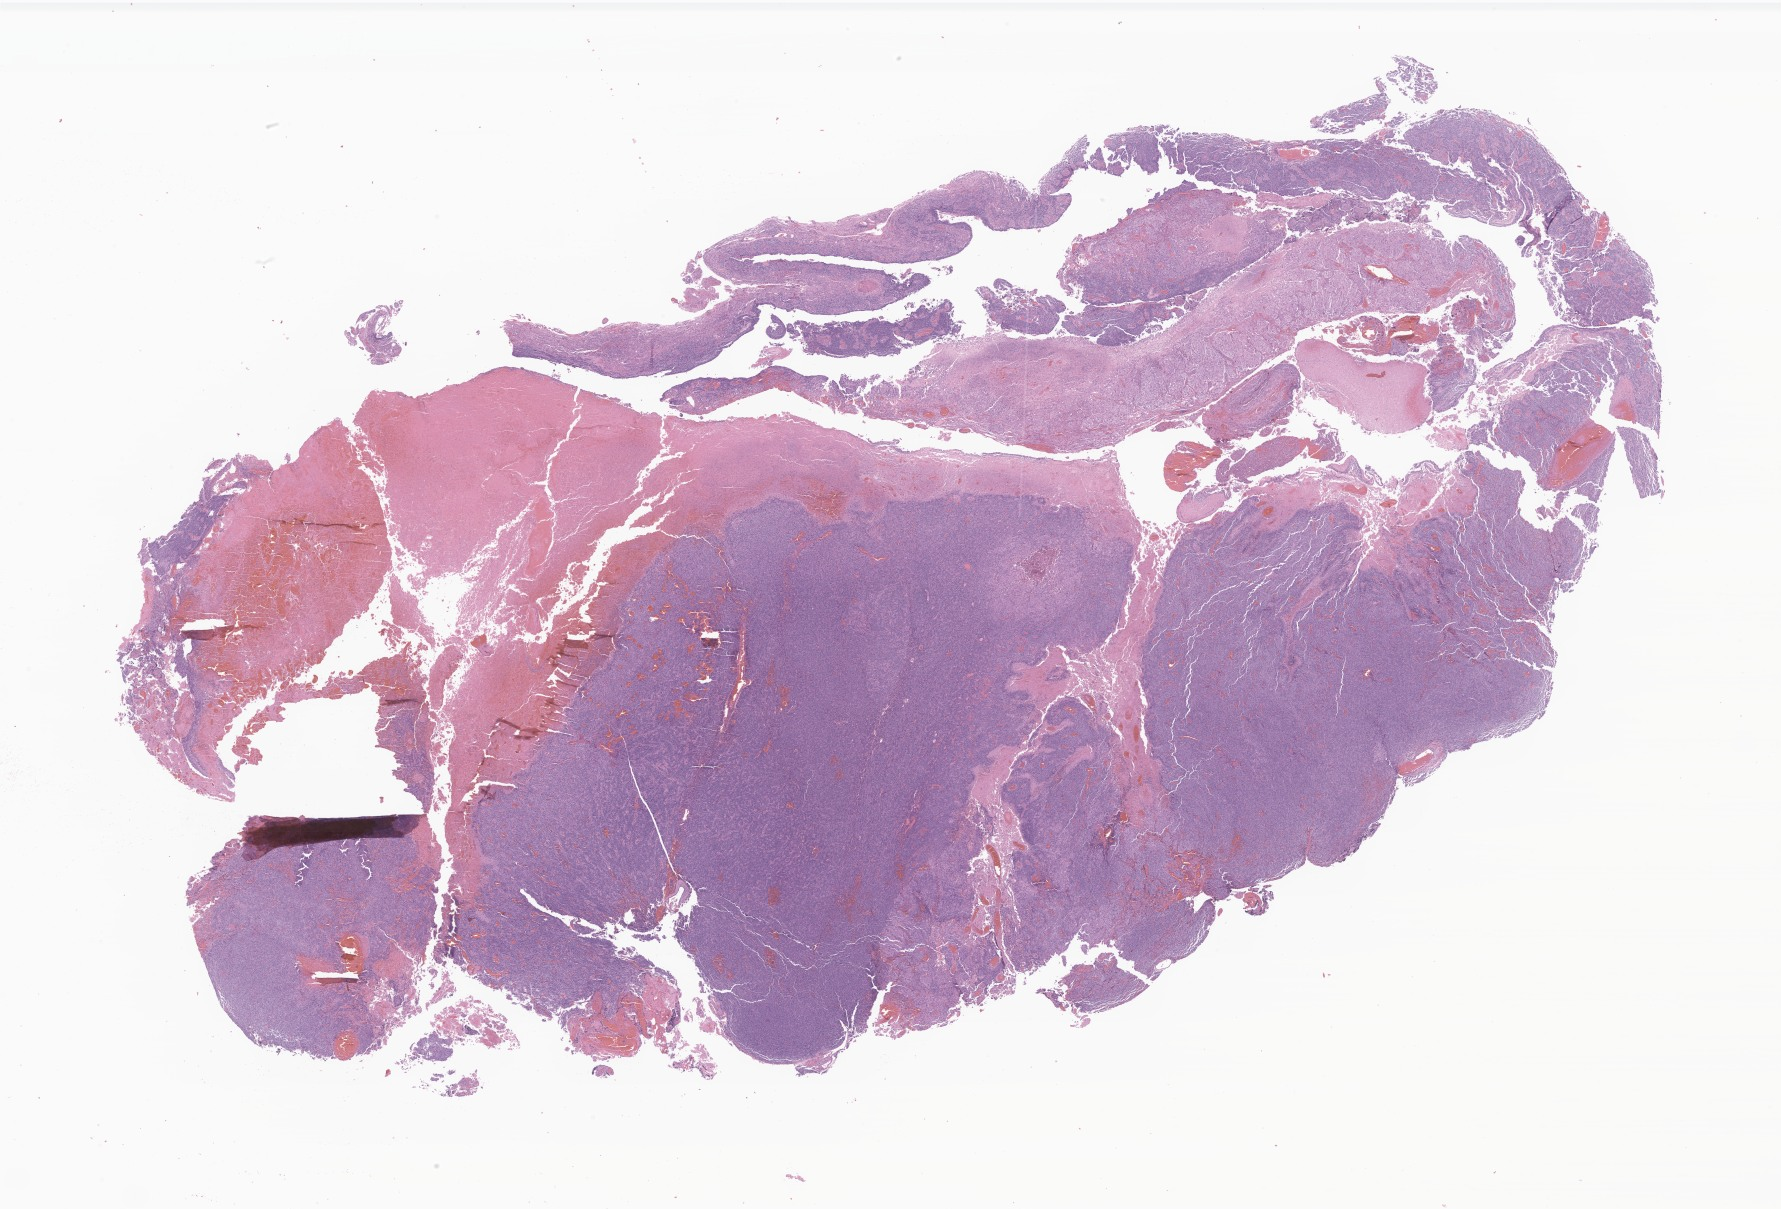
Digitized hematoxylin and eosin (H&E)-stained section of tumor tissue from the brain — shown as a low-resolution overview of the whole scanned area (about 30.0 x 20.4 mm); formalin-fixed, paraffin-embedded (FFPE) tissue. Patient male; age 237 months (19 years 9 months).
Diagnosis (ICD-O-3 morphology term): Ependymoma, anaplastic.